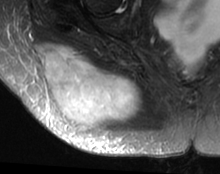
MRI of an extremity soft-tissue mass, one axial slice. Slice 19 of 63 in the series (ordered by position). T2-weighted fat-saturated. MR volume resampled by the dataset authors to the PET/CT grid (not the native acquisition matrix). 220 × 174 image matrix, field of view 215 × 170 mm. Female patient. Case-level facts recorded for this patient, not image findings: histological type: spindle cell suggestive of myxofibrosarcoma; grade: intermediate; site of the primary tumour: right buttock.
Annotated regions visible in this slice (expert contour drawn on MRI and transferred to this co-registered scan by the dataset authors):
- gross tumour volume (mass): bounding box [x1, y1, x2, y2] px = [38, 45, 144, 133]